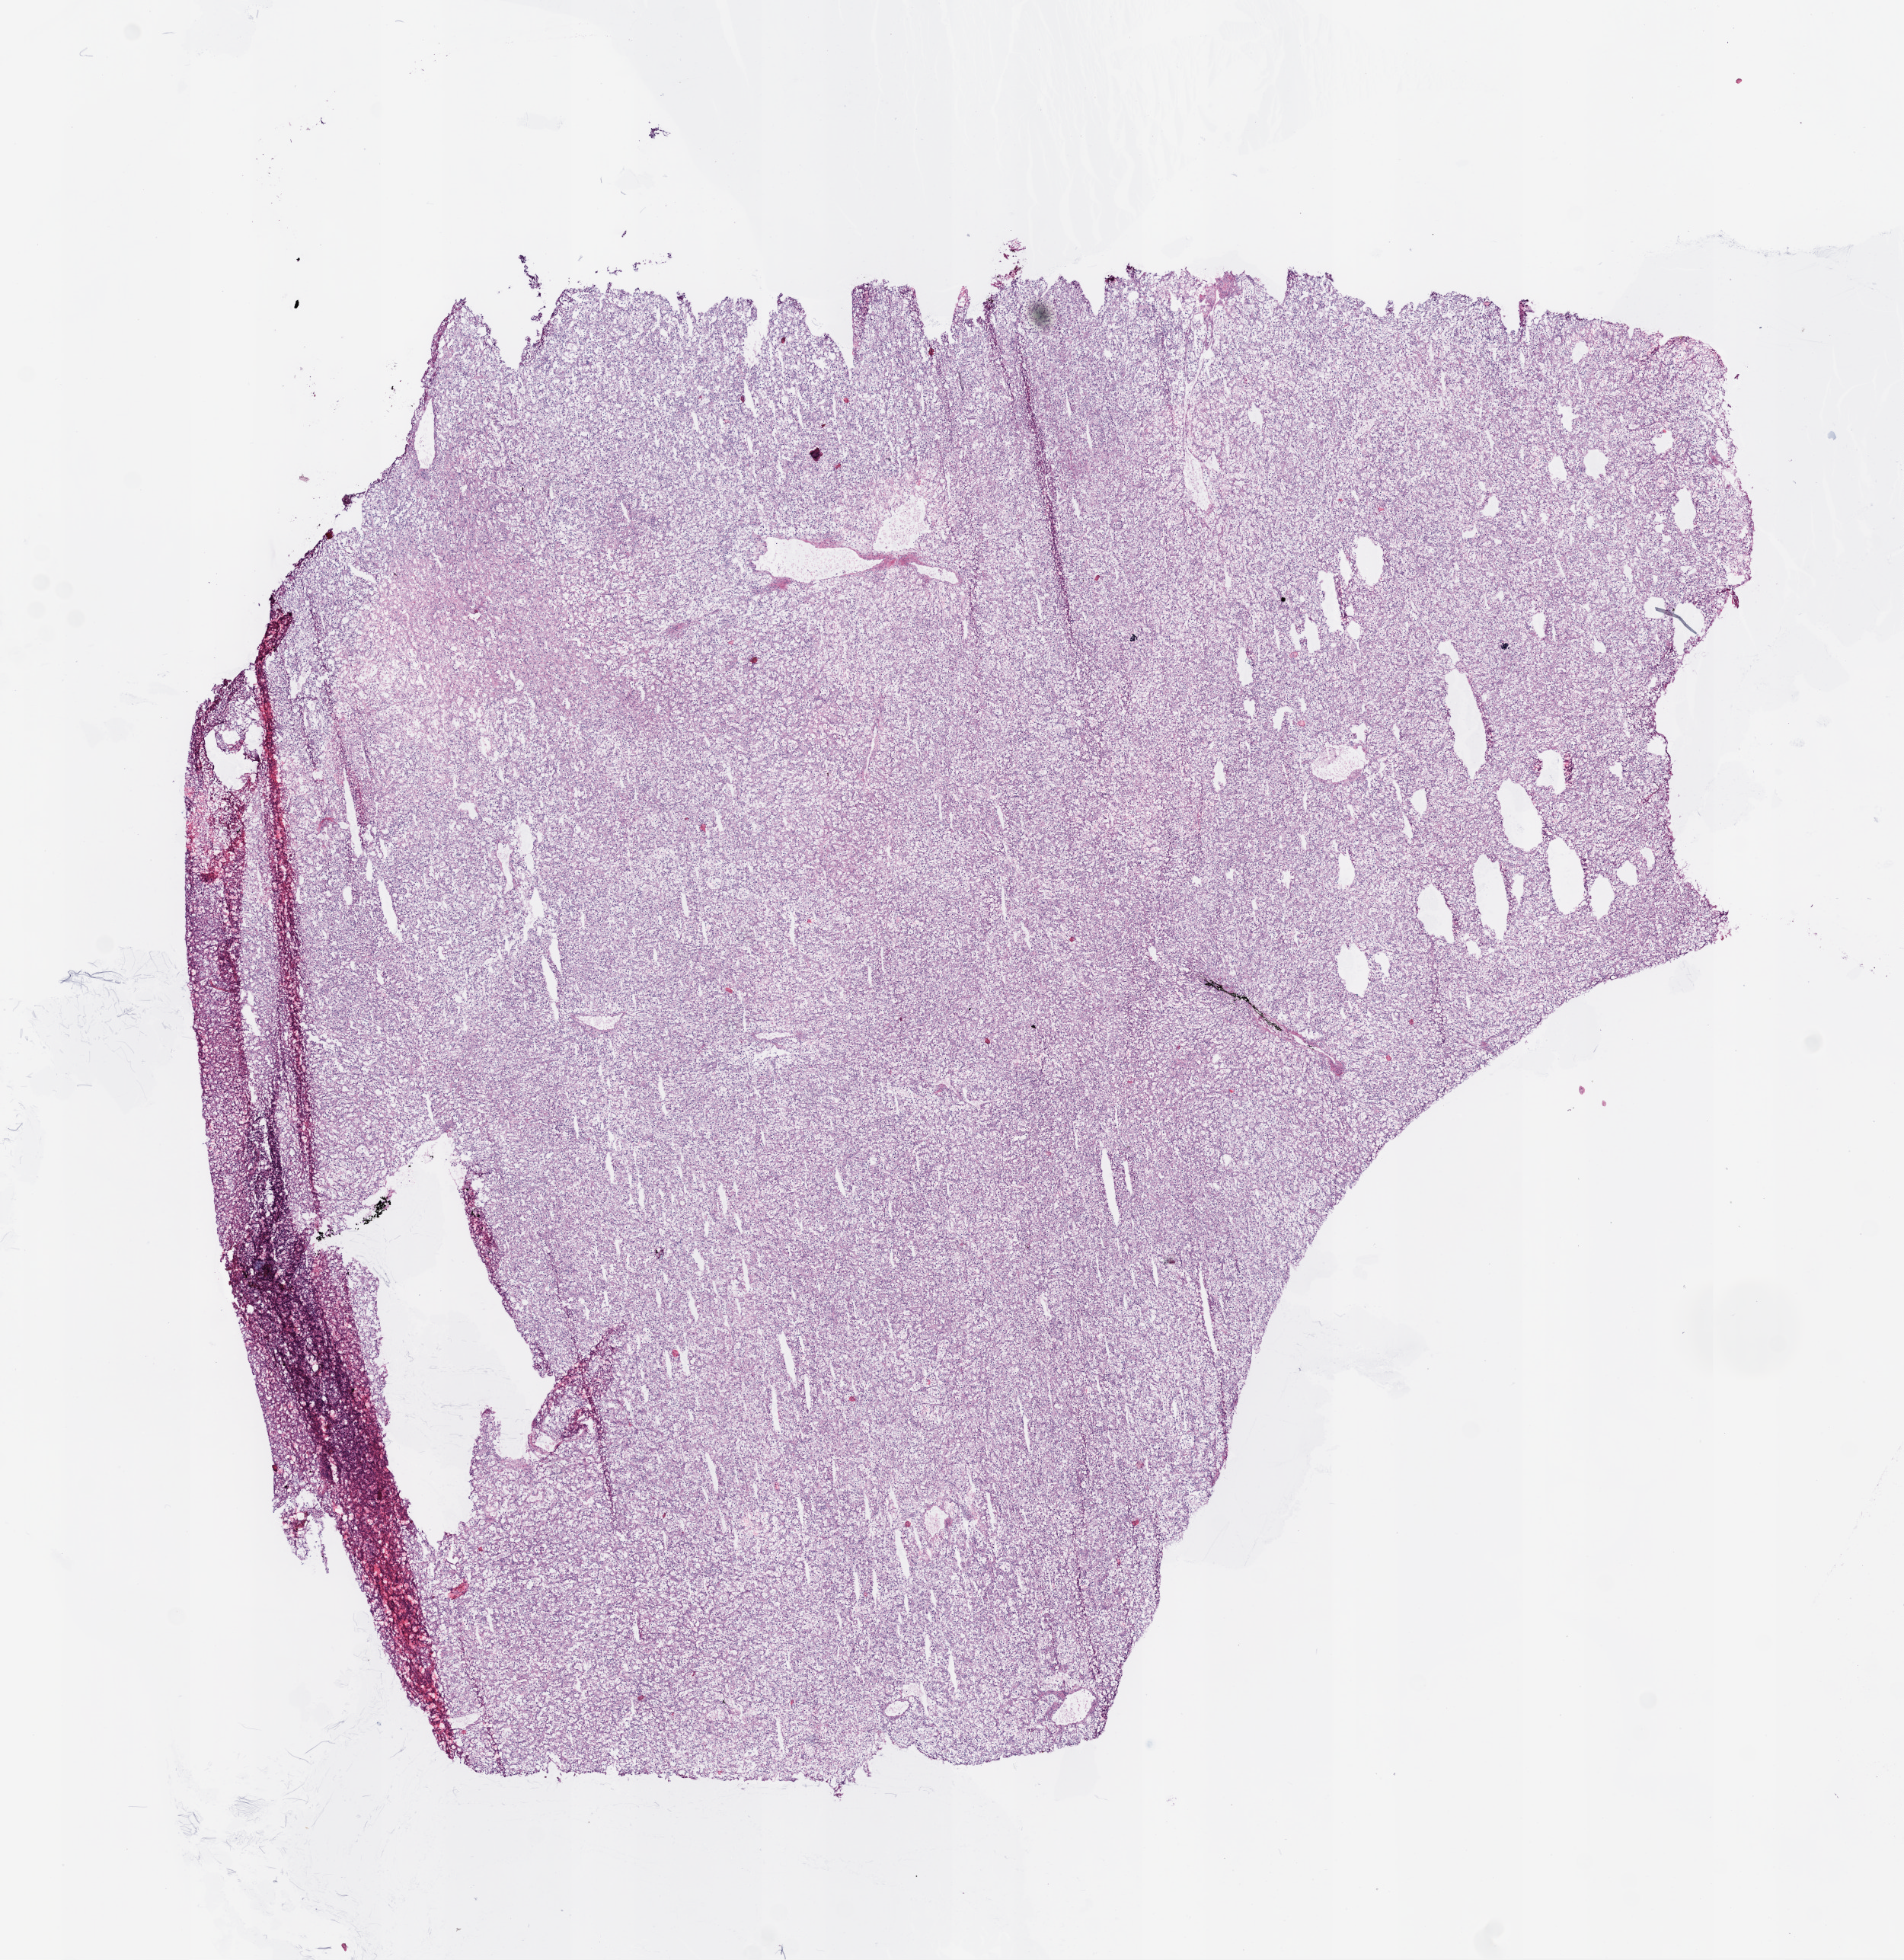
Whole-slide histology image, H&E-stained — whole scanned area (about 10.0 x 10.3 mm) shown as a low-resolution overview; frozen section; sample: primary tumour, kidney. Male patient; age at initial diagnosis 47 years. Histologic grade: G1 (well differentiated). Slide review estimates, as recorded: tumour cells 95%, tumour nuclei 85%, normal cells 0%, stromal cells 5%, necrosis 0%.
• AJCC pathologic stage: I
• histologic diagnosis: Clear cell adenocarcinoma, NOS